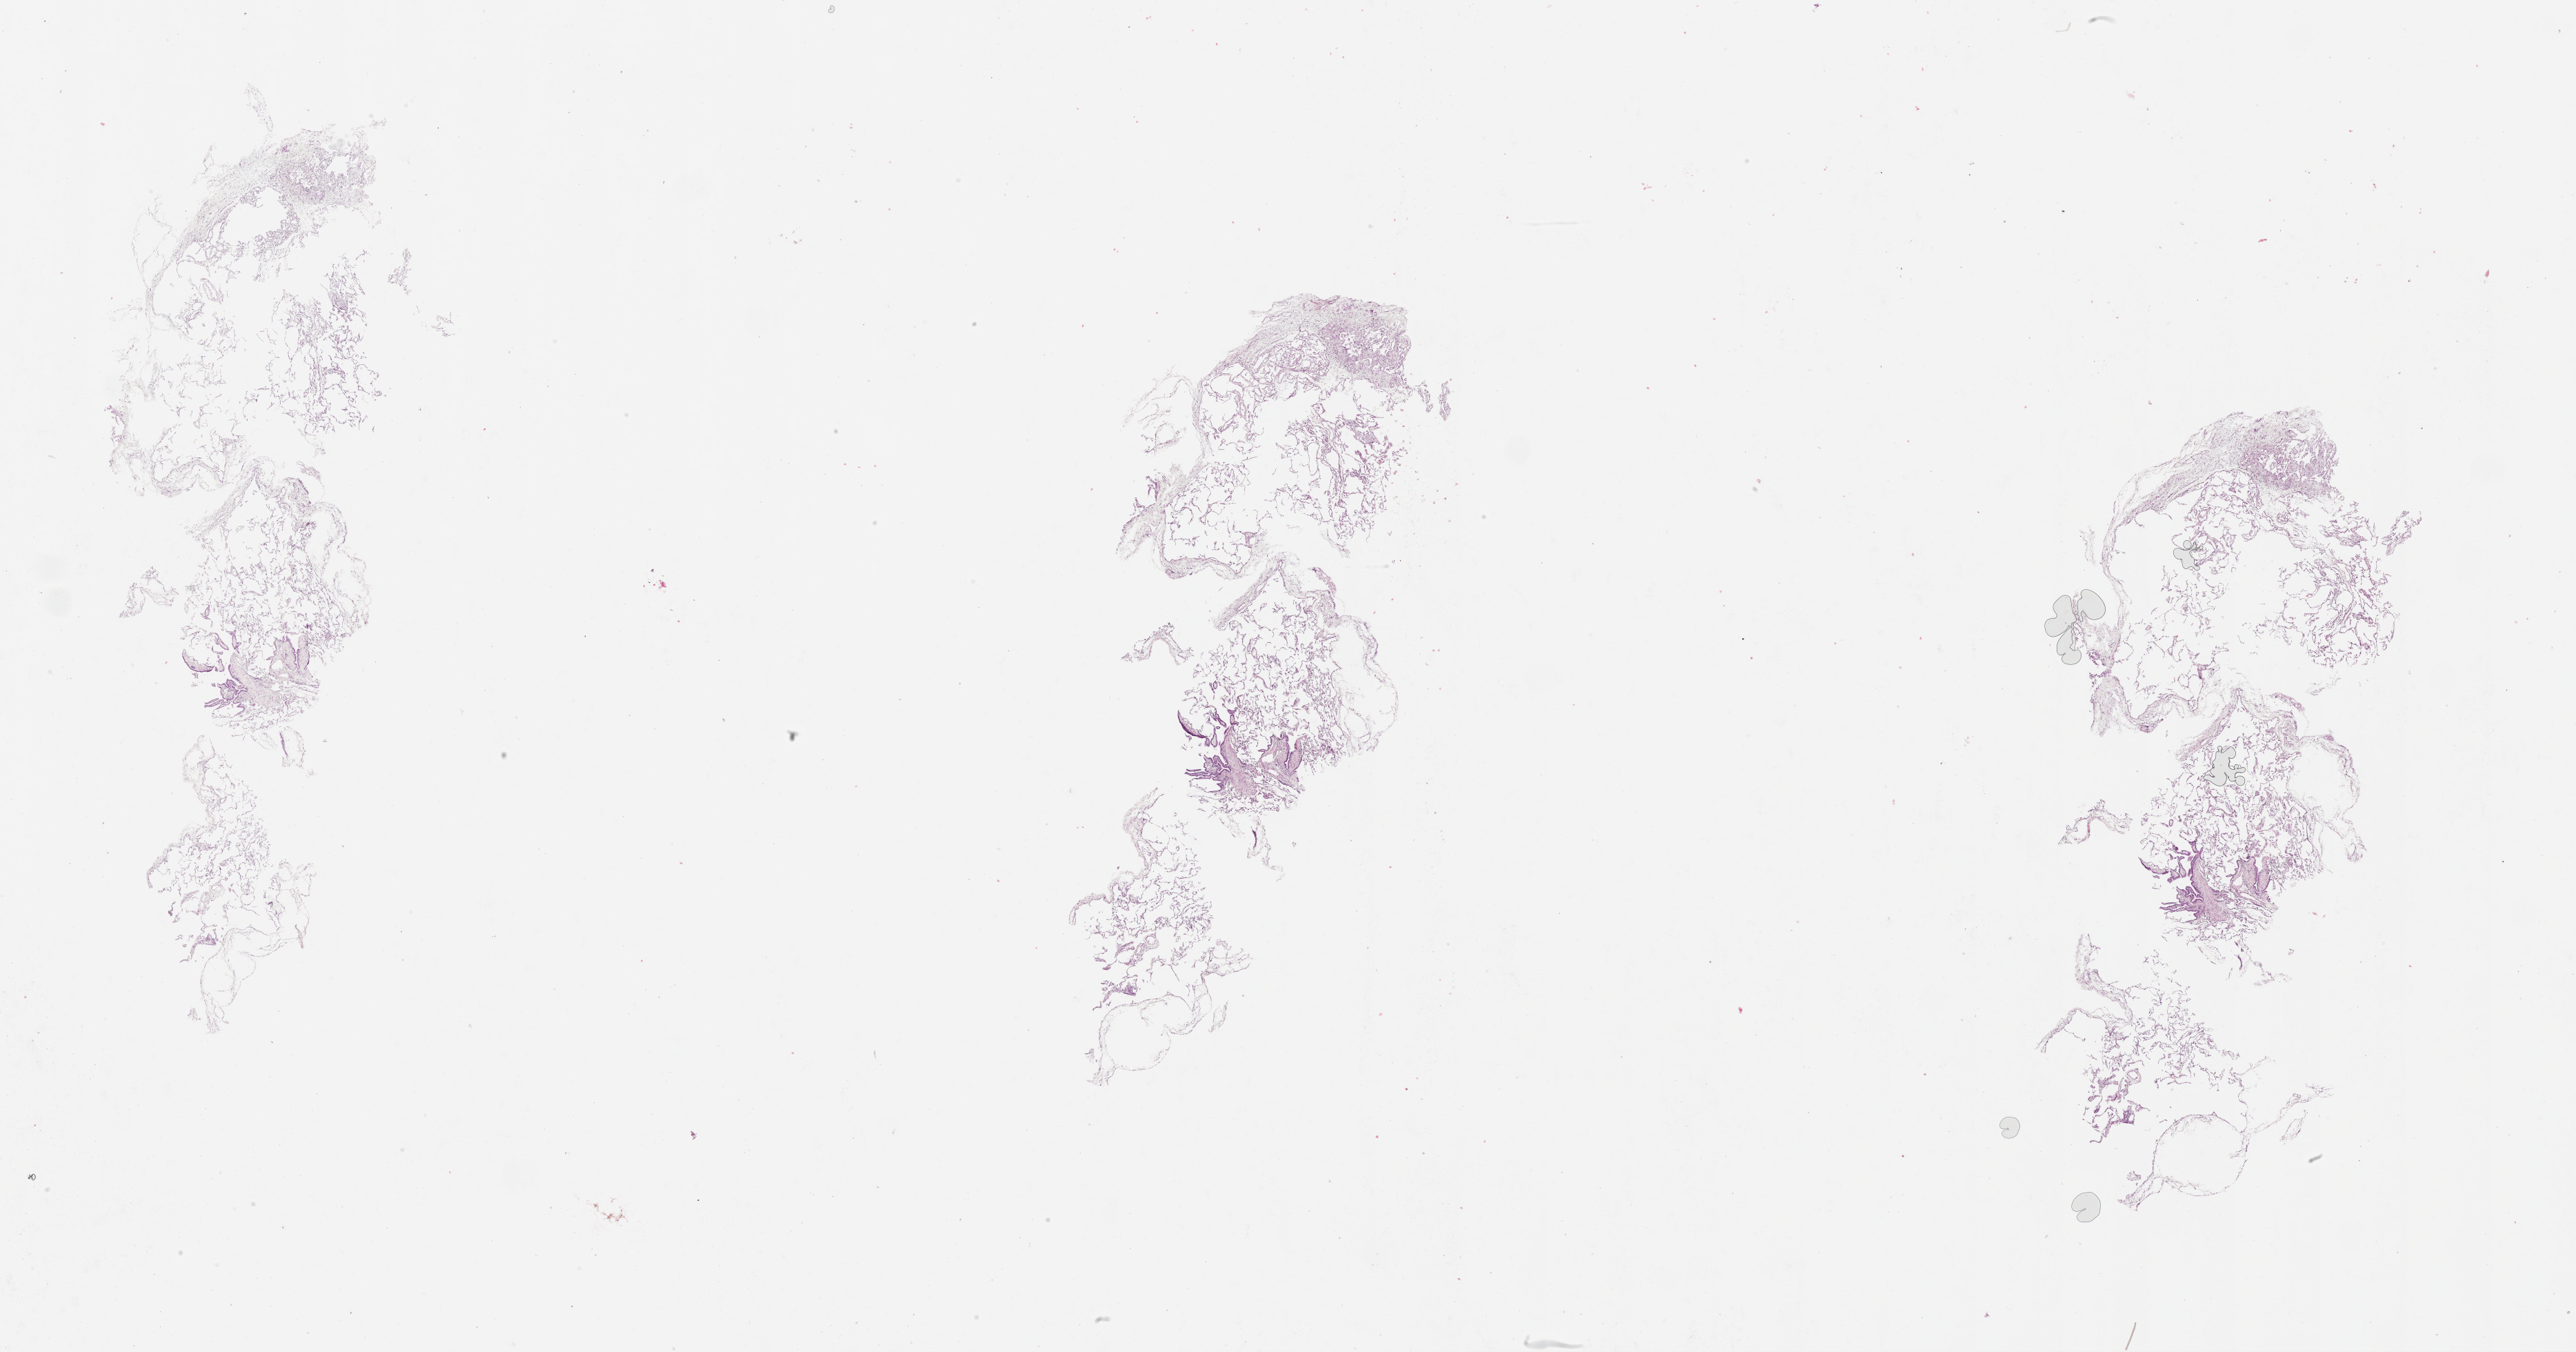
Digitized H&E-stained tissue section (whole slide), shown as a low-resolution overview of the whole scanned area (about 30.1 x 15.8 mm), lung, normal (non-tumour) tissue. 69-year-old male patient.
This section: normal (non-tumour) tissue from the same patient. Patient diagnosis (cohort enrolment): squamous cell carcinoma (lung).